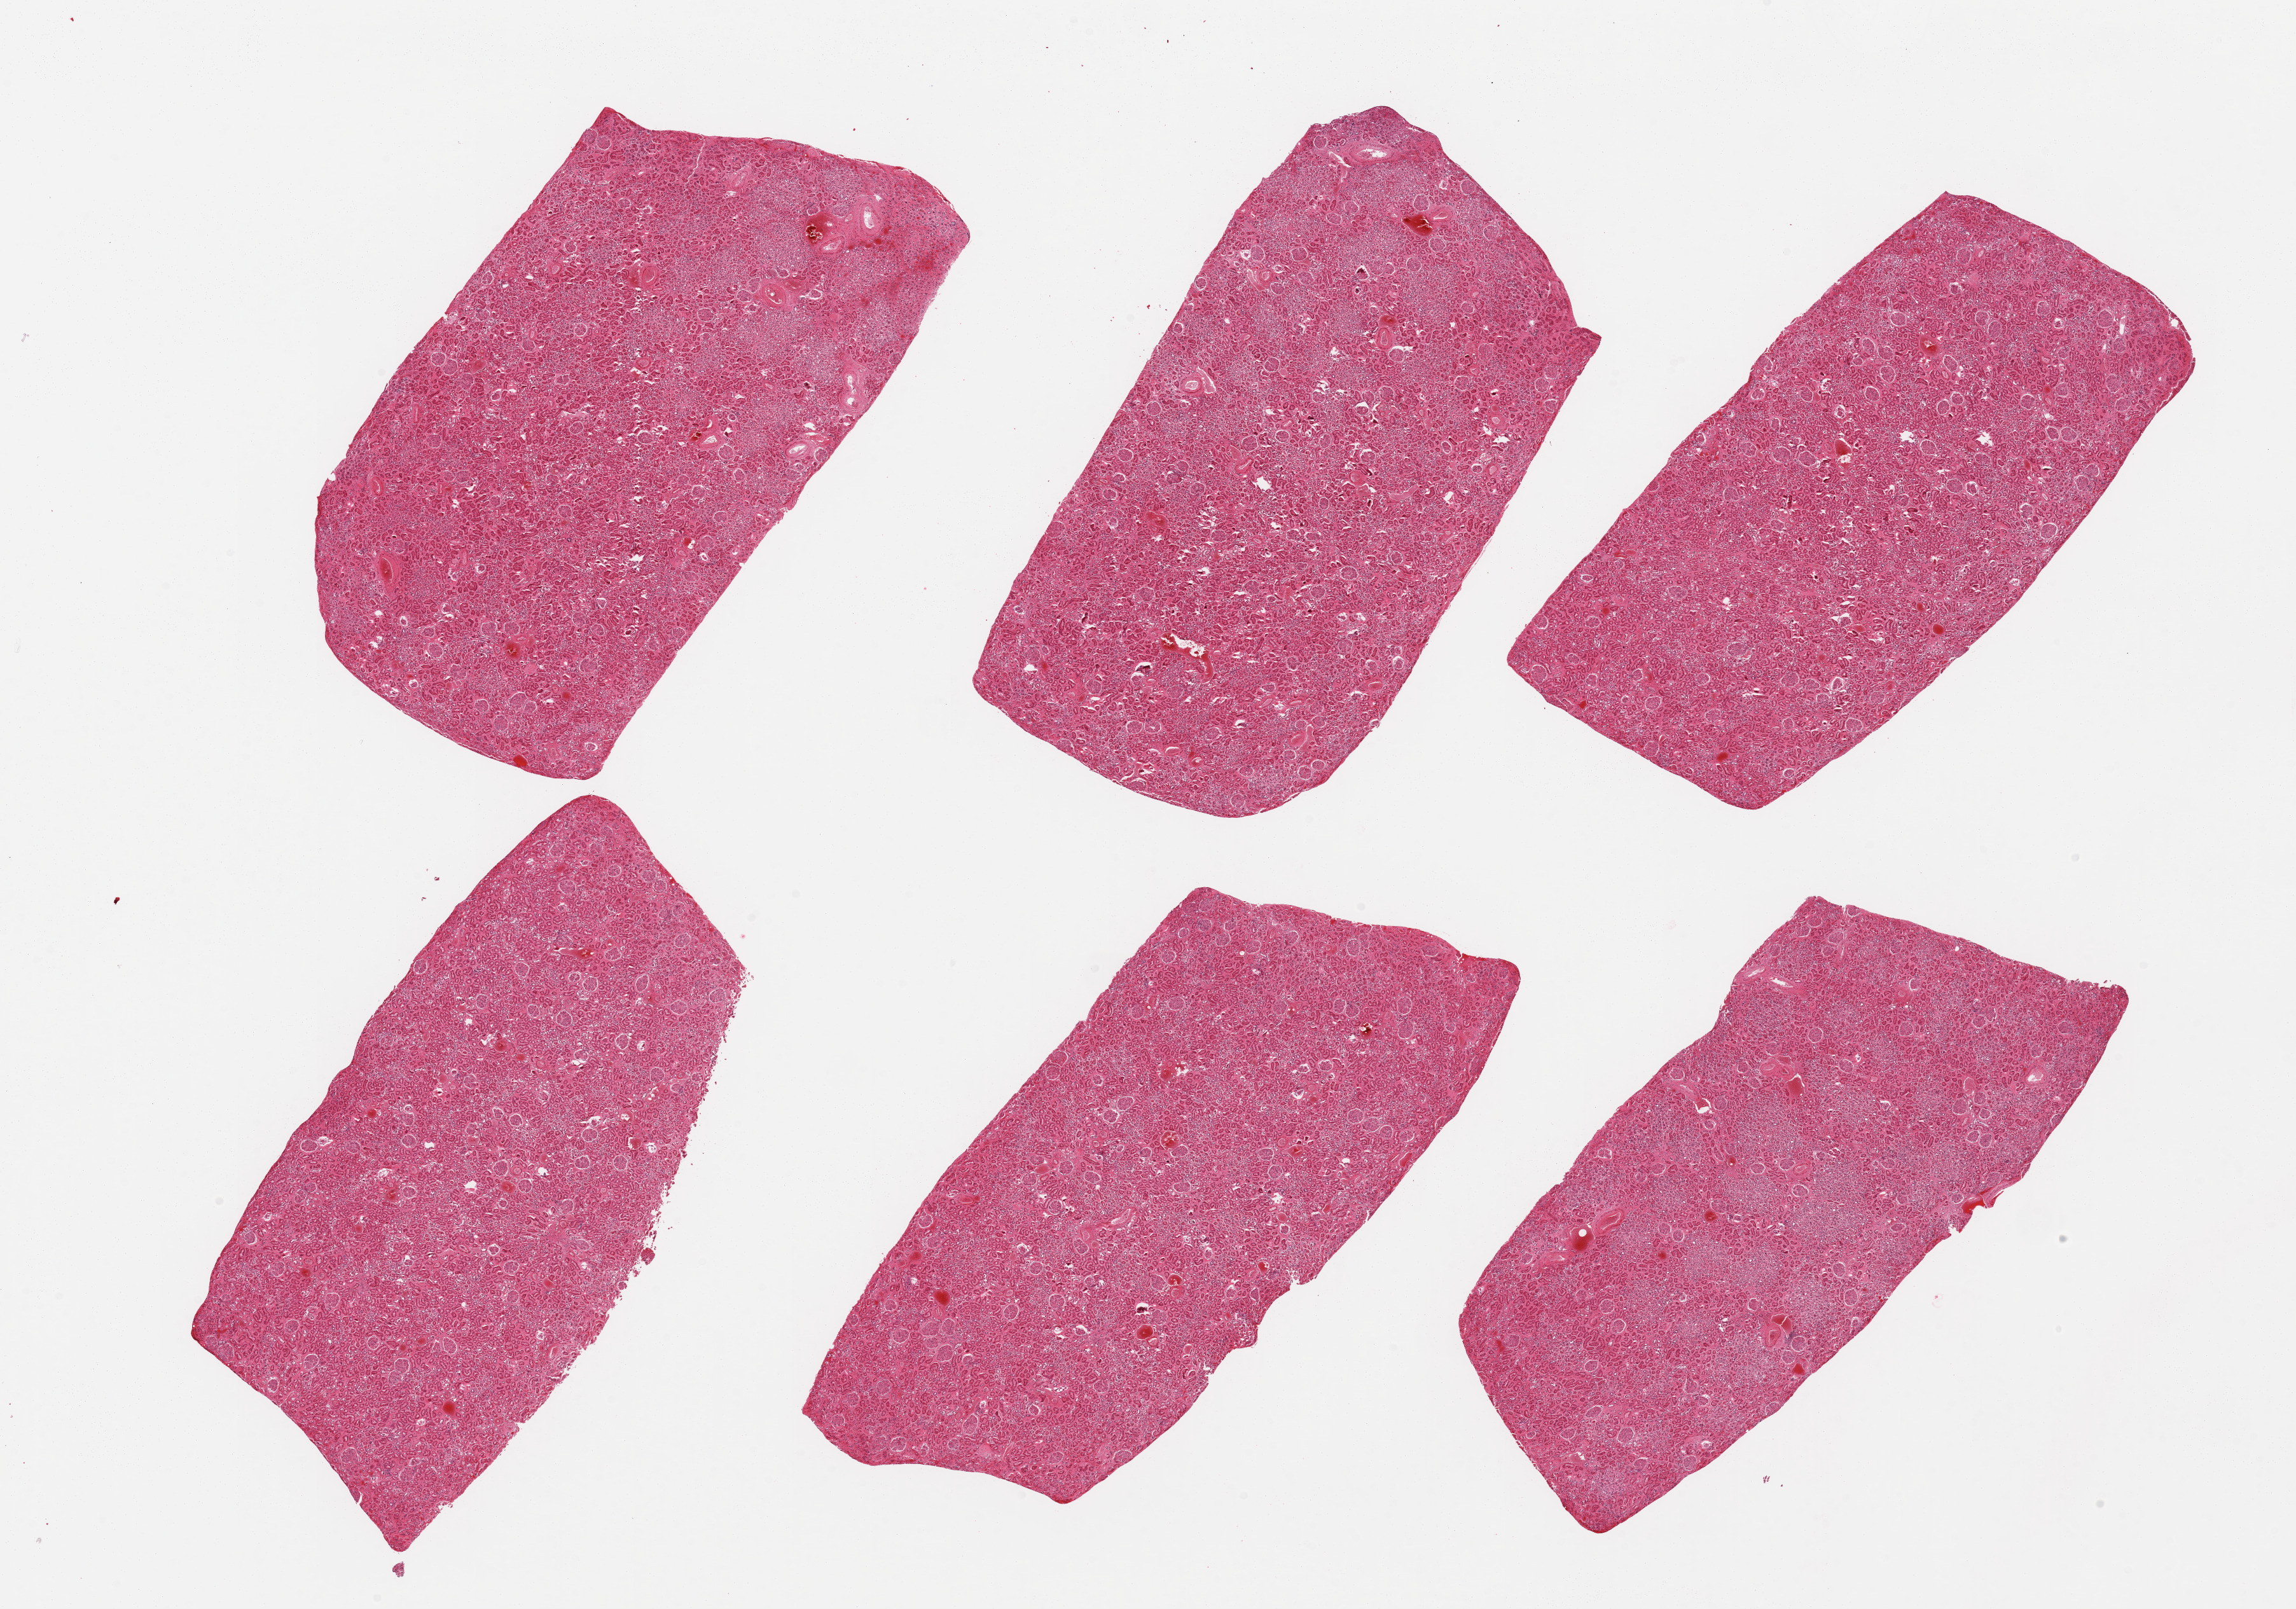
Digitized haematoxylin and eosin-stained section, shown as a low-resolution overview of the whole scanned area (about 28.5 x 20.0 mm, from a 20x scan), PAXgene-fixed paraffin-embedded (PFPE) section, target tissue: renal cortex, tissue donor sample. Donor: male.
Pathologist's review note for this sample: 6 pieces; arteriosclerosis, occasional sclerotic glomeruli.